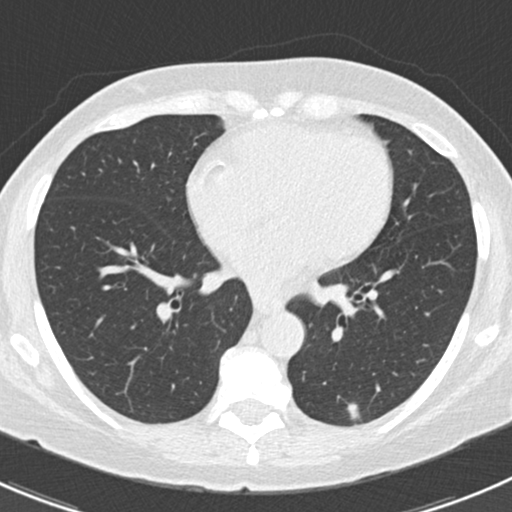
Low-dose screening chest CT, axial slice; second annual screen; lung window (W 1500 / L -600 HU); standard (soft-tissue) reconstruction kernel (B30f); slice 87 of 166 in the series; 512 × 512 image matrix. Female participant, aged 64 years at enrolment.
• Expert-annotated lung lesion, box from (x=329, y=393) to (x=378, y=433) px.
• The exam's reader record, not a measurement of the box and not confirmed to be the same lesion: non-calcified nodule or mass ≥4 mm, left lower lobe, 8 × 3 mm, poorly defined margins, soft tissue attenuation, pre-existing on the prior screen: yes; interval growth: no.
• Later outcome: lung cancer diagnosed 101 days after this screen — adenocarcinoma, NOS, left lower lobe, poorly differentiated (G3), stage IA (AJCC 6th edition), 8 mm at pathology.